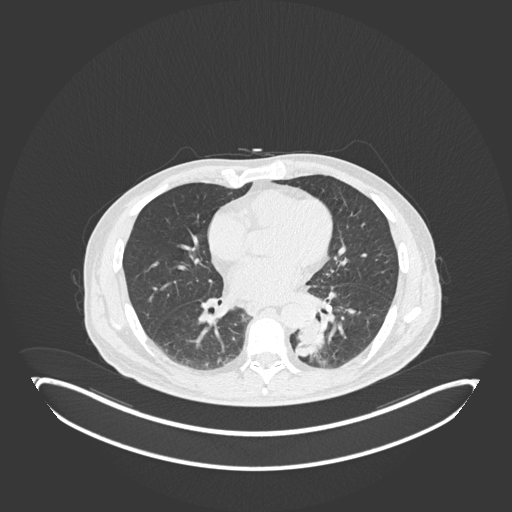
Chest CT, one axial slice; slice 75 of 251 in the series (ordered by position); lung window (W 1500 / L -600 HU); 1 mm slice thickness; 512 × 512 image matrix, field of view 500 × 500 mm. Patient: male, 72 years. Case-level facts recorded for this patient, not image findings: clinical TNM (as recorded): T2b N0 M1.
Outlined on this slice (bounding box drawn by a radiologist):
- lung tumour (recorded histology: adenocarcinoma): bounding box <296,319,327,361> (left, top, right, bottom; pixels)